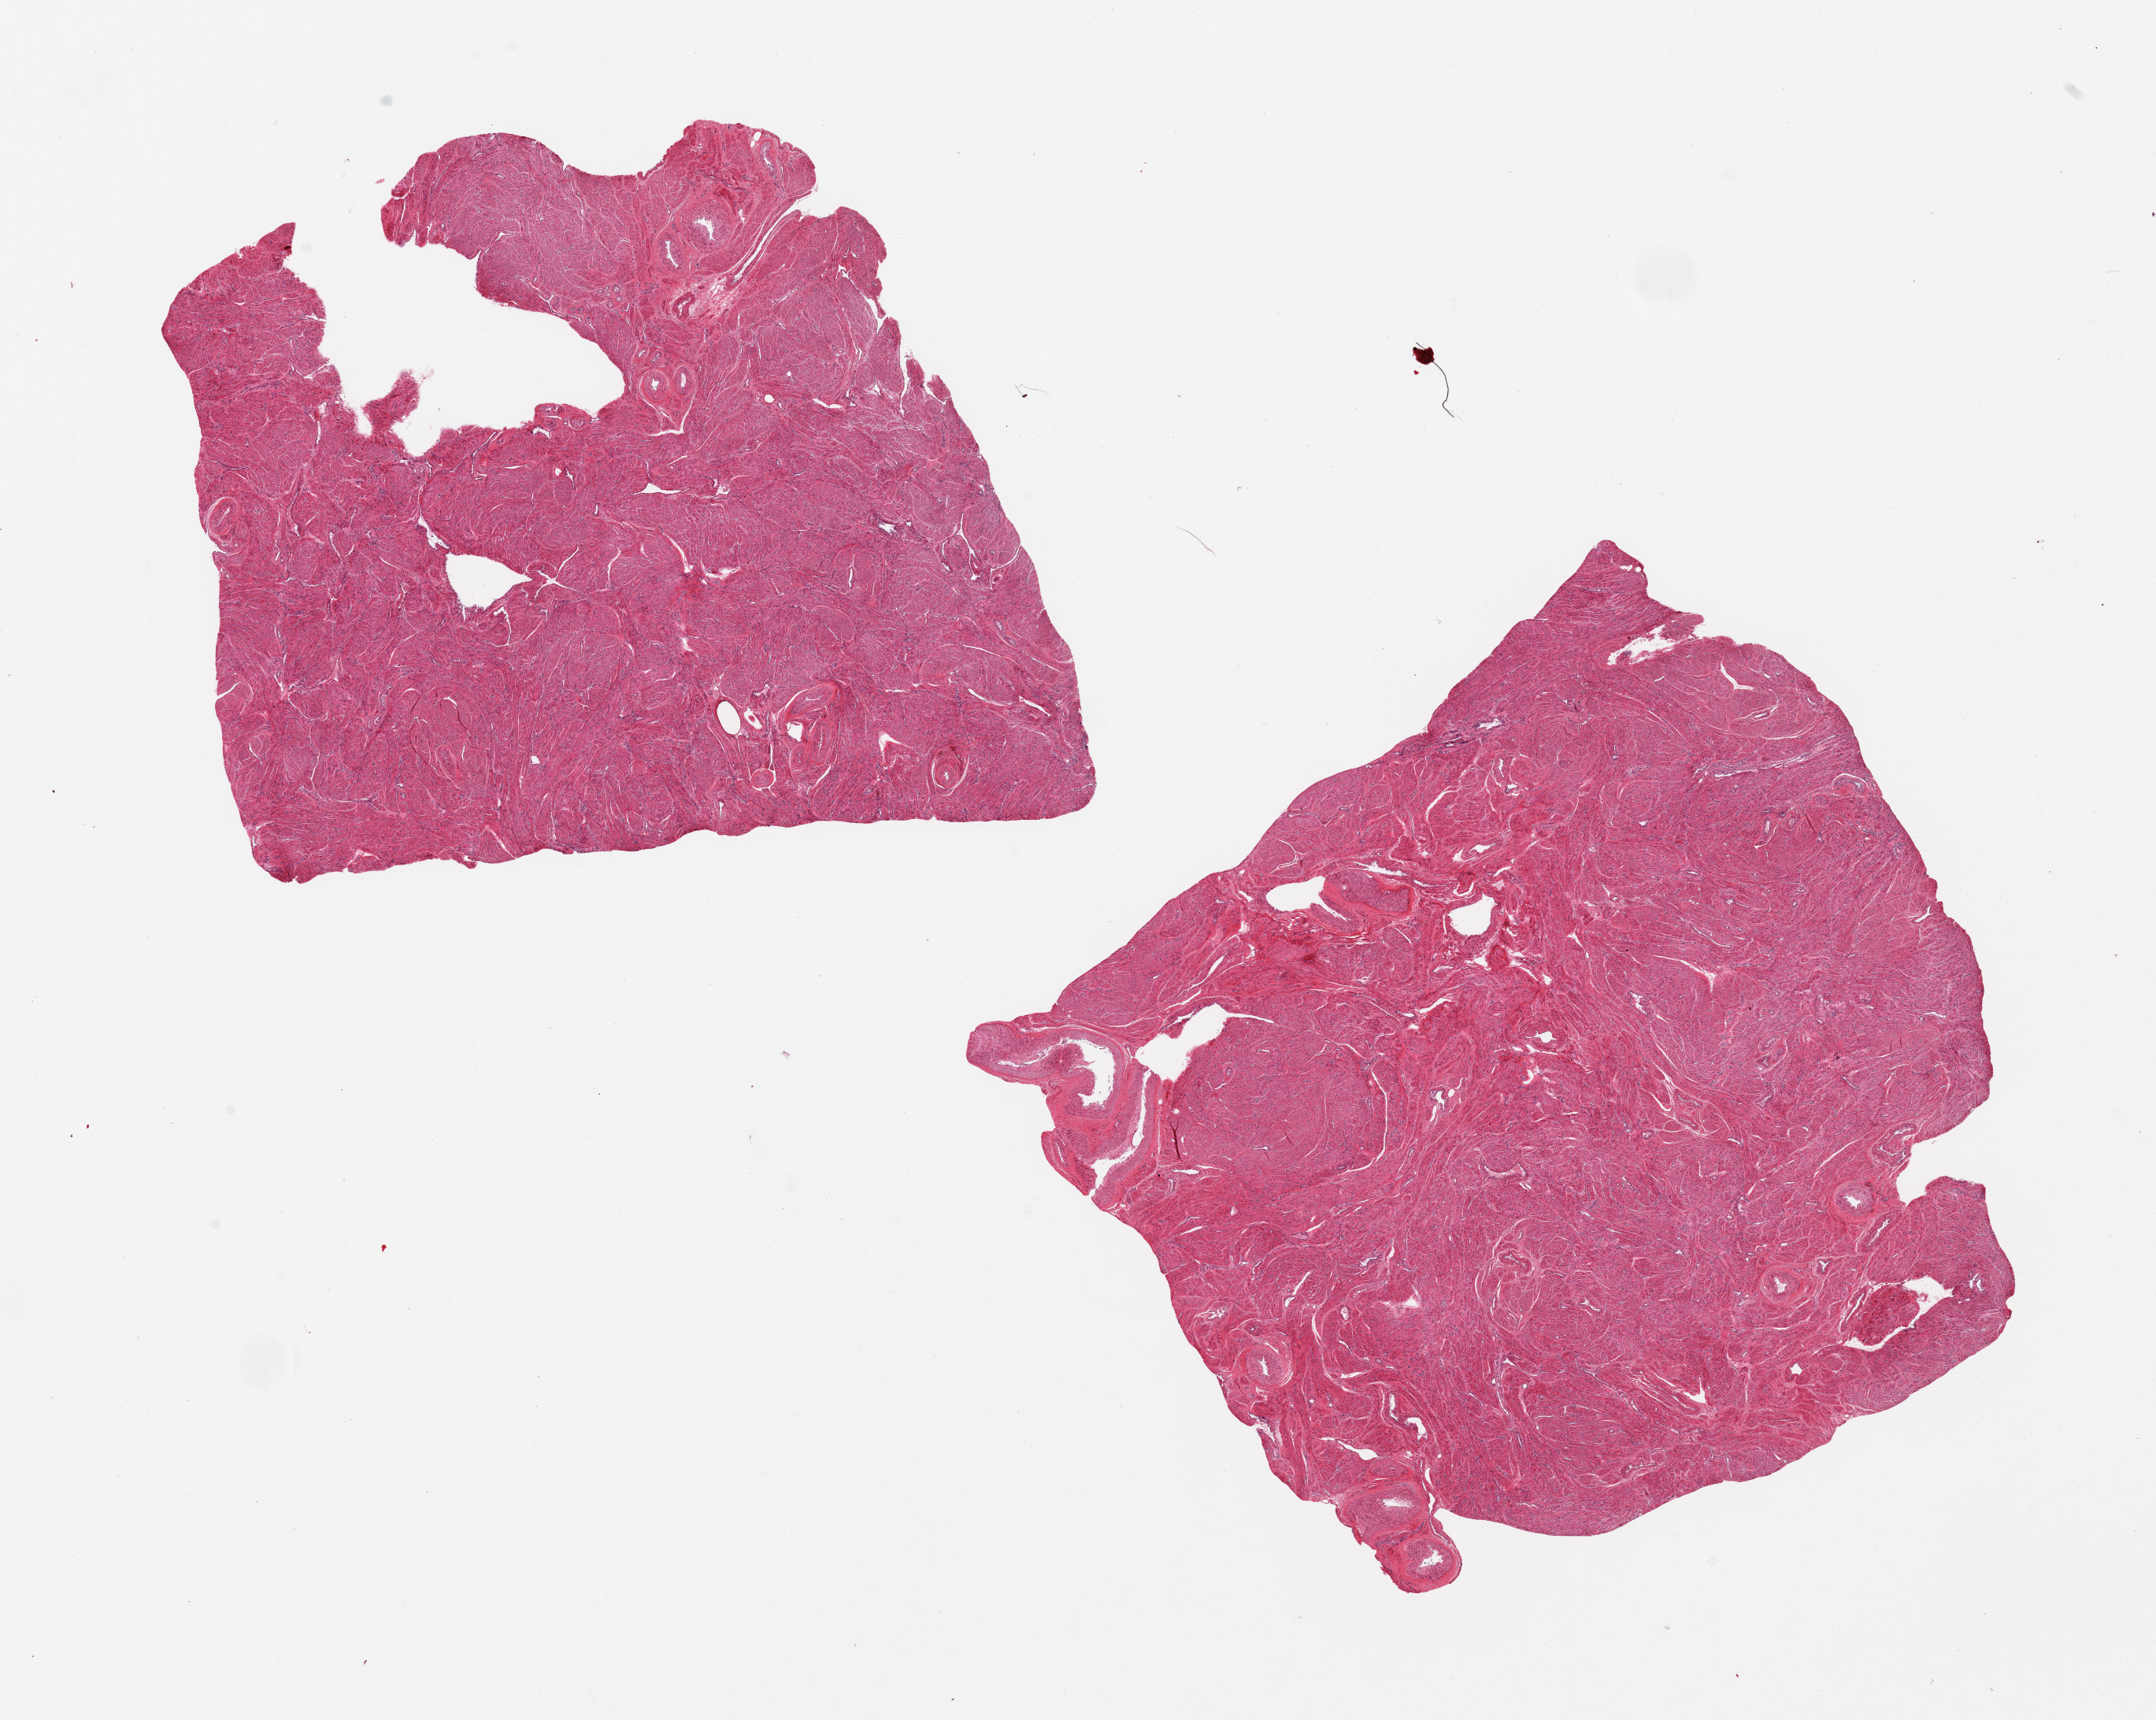
Digitized hematoxylin and eosin (H&E)-stained section, brightfield, a low-resolution overview of the entire scanned area, about 21.7 x 17.3 mm, PAXgene-fixed, paraffin-embedded tissue, sampled site (target tissue): uterus, tissue donor sample. Female donor.
Pathologist's review note for this sample: 2 pieces, all myometrium.